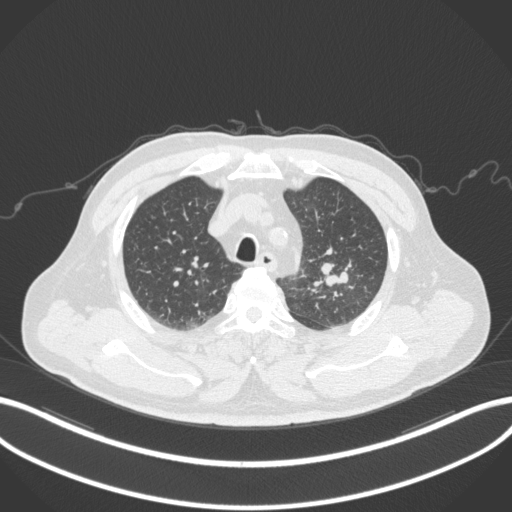
Chest CT, one axial slice. Slice 239 of 286 in the series (ordered by position). Reconstruction kernel B31f. 120 kVp. Lung window (W 1500 / L -600 HU). 512 × 512 image matrix, field of view 400 × 400 mm. Patient: male, 67 years. Case-level facts recorded for this patient, not image findings: clinical TNM (as recorded): T2a N1 M0; histopathological grade: G3.
Annotated regions visible in this slice (rectangle marked by the reading radiologist):
- lung tumour (recorded histology: adenocarcinoma): bounding box (x1, y1, x2, y2) in pixels: (319, 258, 352, 288)